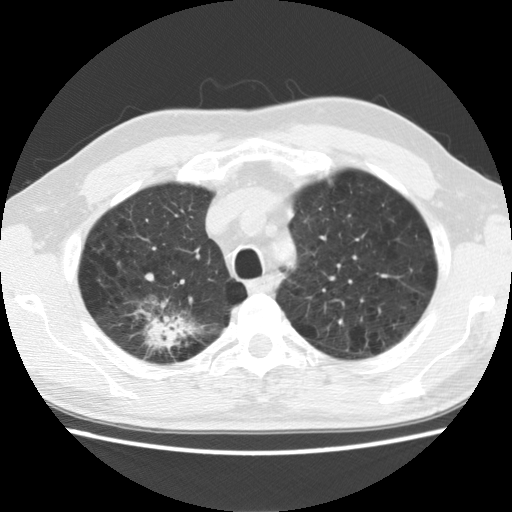
Low-dose screening chest CT, one axial slice; position 109 of 142 along the scan axis; 120 kVp; lung window (W 1500 / L -600 HU); 2.5 mm slice thickness; 512 × 512 image matrix, field of view 340 × 340 mm.
Annotated regions visible in this slice (outlined manually by an expert reader):
- lesion 1 (tumor, upper lobe of right lung): bounding box [x1, y1, x2, y2] px = [147, 322, 176, 348]